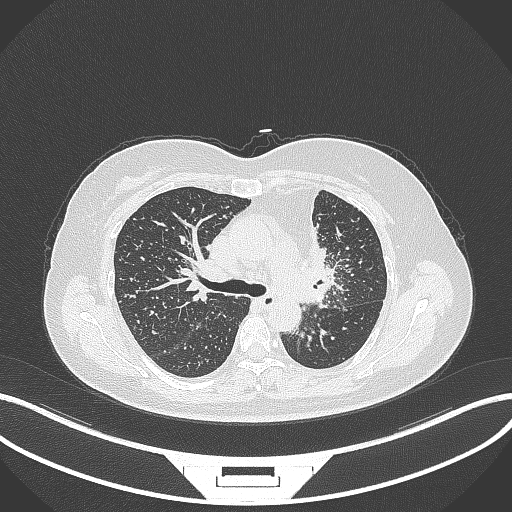
Chest CT, one axial slice. Slice 216 of 348 in the series (ordered by position). 120 kVp. Lung window (W 1500 / L -600 HU). 1 mm slice thickness. 512 × 512 image matrix, field of view 400 × 400 mm. Female patient, age 49 years. From the clinical record (not read from this slice): clinical TNM (as recorded): T1c N0 M1.
Structures marked on this image (bounding box drawn by a radiologist):
- lung tumour (recorded histology: adenocarcinoma): bounding box <304,229,337,307> (left, top, right, bottom; pixels)